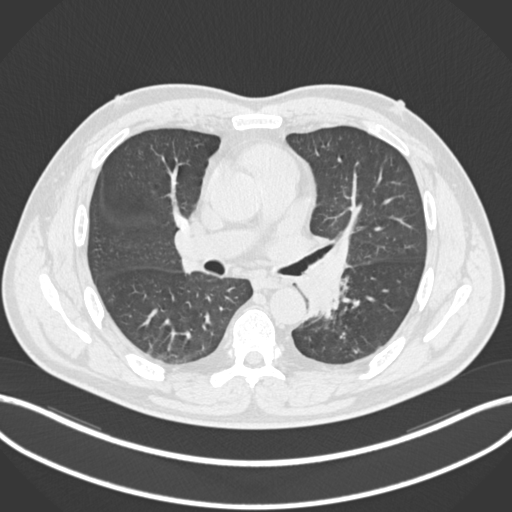
Chest CT, one axial slice; slice 127 of 223 in the series (ordered by position); reconstruction kernel B30f; 120 kVp; lung window (W 1500 / L -600 HU); 1 mm slice thickness; 512 × 512 image matrix, field of view 400 × 400 mm. Patient: male, 50 years. Case-level facts recorded for this patient, not image findings: clinical TNM (as recorded): T2a N3 M0.
Structures marked on this image (rectangle marked by the reading radiologist):
- lung tumour (recorded histology: squamous cell carcinoma): box from (x=293, y=236) to (x=355, y=318) px